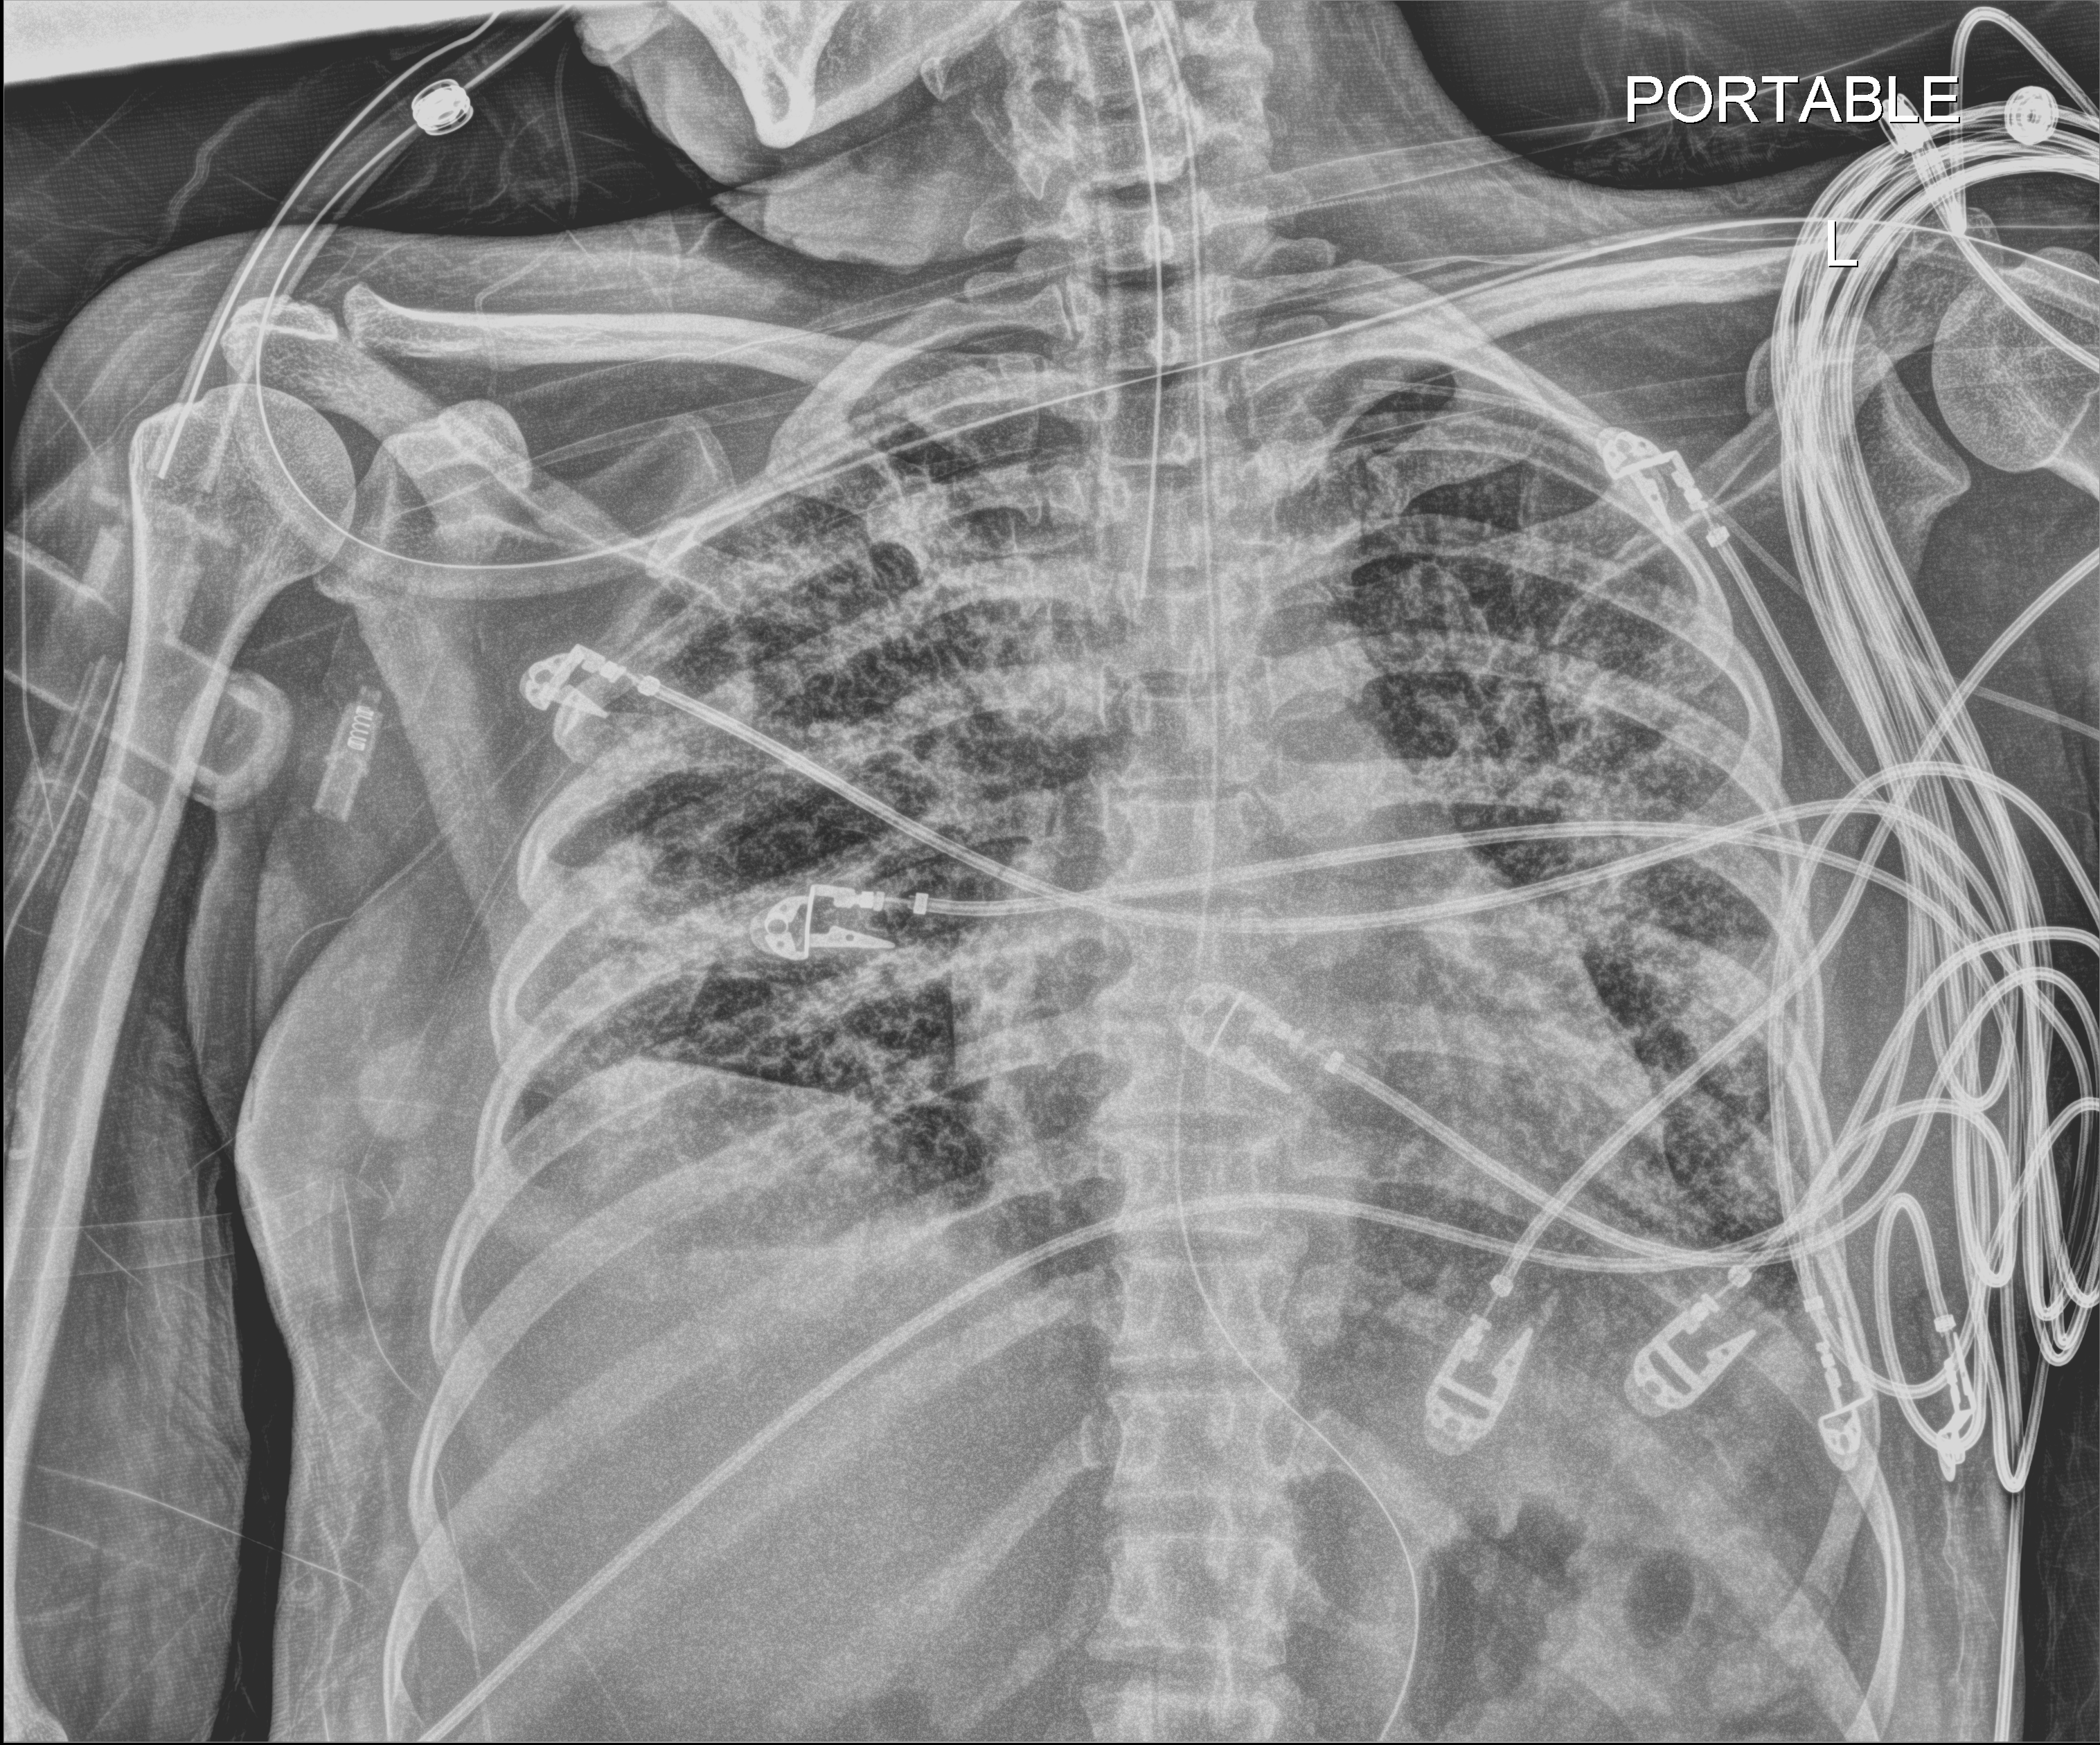
Chest X-ray (portable). Female patient hospitalised with COVID-19, age 18–59 years.
From the hospital-stay record, not from the radiograph (when in the stay this image was taken is not recorded): length of hospital stay: 71 days; admitted to intensive care during this hospital stay: yes; other chronic lung disease (admission record): no.